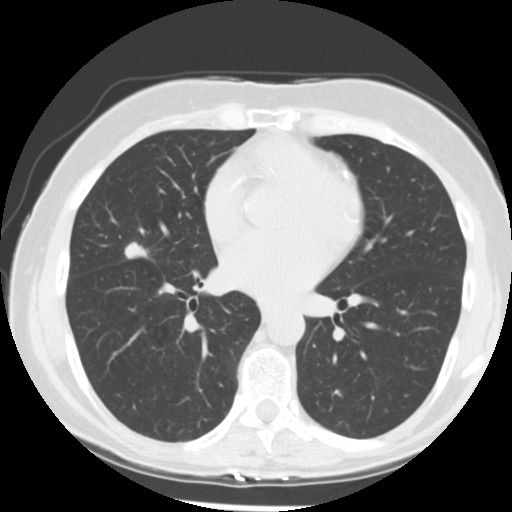
Low-dose screening chest CT, one axial slice; slice 130 of 255 in the series (ordered by position); reconstruction kernel STANDARD; 120 kVp; lung window (W 1500 / L -600 HU); 2.5 mm slice thickness; 512 × 512 image matrix.
Annotated regions visible in this slice (outlined manually by an expert reader):
- lesion 1 (tumor, middle lobe of right lung): bounding box (x1, y1, x2, y2) in pixels: (125, 242, 148, 259)